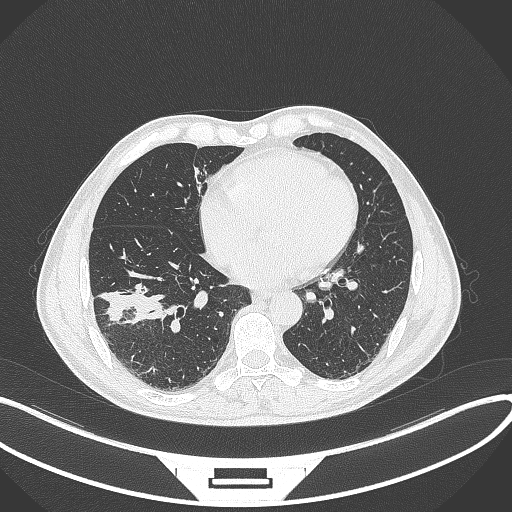
Chest CT, one axial slice; 120 kVp; lung window (W 1500 / L -600 HU); 1 mm slice thickness; 512 × 512 image matrix, field of view 400 × 400 mm. Patient: male, 58 years. Case-level facts recorded for this patient, not image findings: clinical TNM (as recorded): T3 N0 M0; histopathological grade: G2.
Annotated regions visible in this slice (bounding box drawn by a radiologist):
- lung tumour (recorded histology: squamous cell carcinoma): box from (x=98, y=286) to (x=168, y=331) px